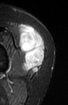
MRI of an extremity soft-tissue mass, one axial slice; slice 33 of 52 in the series (ordered by position); STIR; MR volume resampled by the dataset authors to the PET/CT grid (not the native acquisition matrix); 68 × 105 image matrix. Female patient. Case-level facts recorded for this patient, not image findings: histological type: spindle cell suggestive of biphasic synovial sarcoma; grade: intermediate; site of the primary tumour: left knee.
Outlined on this slice (expert contour drawn on MRI and transferred to this co-registered scan by the dataset authors):
- gross tumour volume including surrounding oedema: box from (x=19, y=25) to (x=45, y=71) px
- gross tumour volume (mass): (x=19, y=25)–(x=45, y=71)